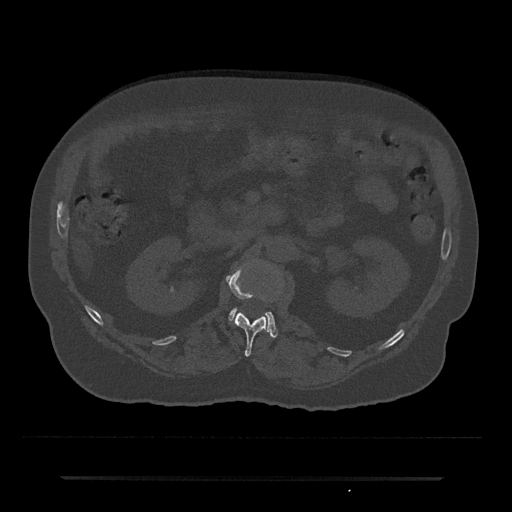
CT including the spine, one axial slice. 120 kVp. Bone window (W 1800 / L 400 HU). 512 × 512 image matrix, field of view 437 × 437 mm. Patient: male, 69 years. Case-level facts recorded for this patient, not image findings: primary cancer: prostate.
Outlined on this slice (semi-automatically segmented with operator editing):
- L1 vertebra: bounding box (x1, y1, x2, y2) in pixels: (226, 264, 270, 357)
- L2 vertebra: (229, 308, 278, 338)